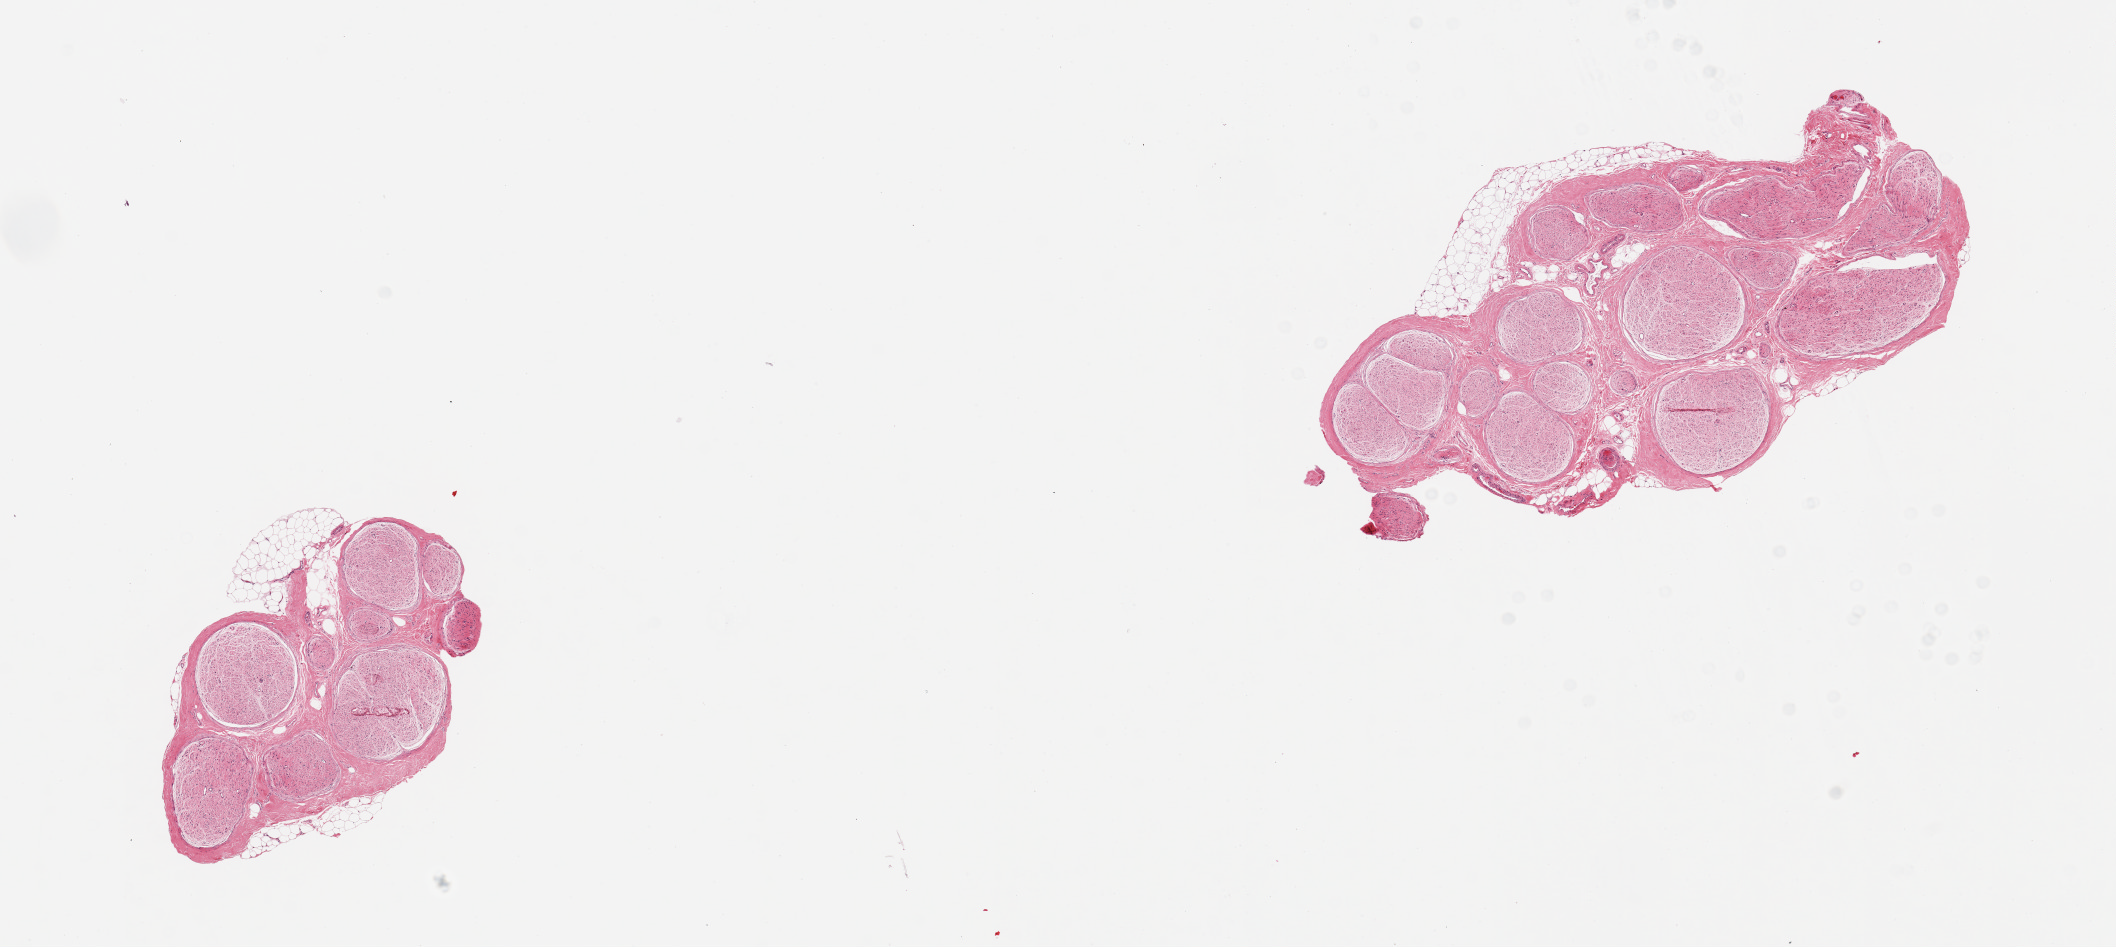
Whole-slide image, haematoxylin and eosin stain — low-resolution overview of the scanned area, about 16.7 x 7.5 mm. Male donor.
Specimen: PAXgene-fixed, paraffin-embedded tissue; sampled site (target tissue): tibial nerve; tissue donor sample.